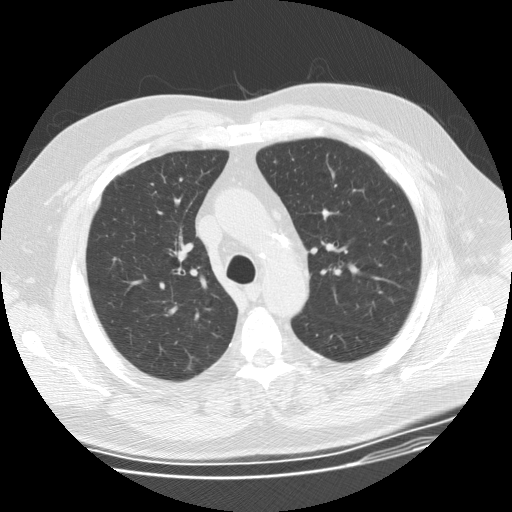
Axial slice from a low-dose chest CT screening exam; third screening round (two years after baseline); lung window (W 1500 / L -600 HU); 2.5 mm slice thickness; standard (soft-tissue) reconstruction kernel (STANDARD); 512 × 512 image matrix. Male, age 62 years at enrolment.
- Expert reader's lesion annotation, bounding box <175,348,212,379> (left, top, right, bottom; pixels).
- The exam's reader record, not a measurement of the box and not confirmed to be the same lesion: non-calcified nodule or mass ≥4 mm, right upper lobe, 10 × 10 mm, poorly defined margins, ground glass attenuation, pre-existing on the prior screen: yes; interval growth: yes.
- Later outcome: lung cancer diagnosed 48 days after this screen — bronchiolo-alveolar adenocarcinoma, NOS, right upper lobe, well differentiated (G1), stage IA (AJCC 6th edition), 12 mm at pathology.